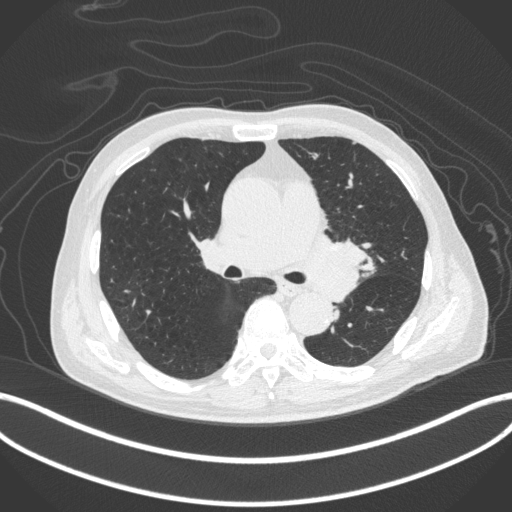
Chest CT, one axial slice. 120 kVp. Lung window (W 1500 / L -600 HU). 1 mm slice thickness. 512 × 512 image matrix, field of view 400 × 400 mm. Patient: male, 77 years. Case-level facts recorded for this patient, not image findings: clinical TNM (as recorded): T3 N1 M0.
Outlined on this slice (rectangle marked by the reading radiologist):
- lung tumour (recorded histology: adenocarcinoma): box from (x=306, y=234) to (x=370, y=304) px